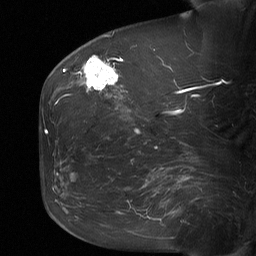
Breast MRI (dynamic contrast-enhanced), one sagittal slice; slice 23 of 64 in the series (ordered by position); dynamic contrast-enhanced study with each time point stored as its own series, time point 2 of 3 at this slice position (early post-contrast, ordered by acquisition time); 1.5 T; TE 4.8 ms, TR 27 ms; 2 mm slice thickness; 256 × 256 image matrix, field of view 200 × 200 mm. Female patient, age 60 years. From the clinical record (not read from this slice): setting: breast cancer imaged before/during neoadjuvant chemotherapy; receptor status: HR-positive, HER2-negative.
Structures marked on this image (semi-automatic segmentation, software-assisted and operator-edited):
- analysis volume of interest (the breast-tissue region the enhancement analysis was run in; not a lesion): bounding box (x1, y1, x2, y2) in pixels: (79, 50, 122, 99)
- tumour enhancement mask (voxels above the 90 % enhancement threshold inside the analysis volume of interest): (84, 56, 118, 90)